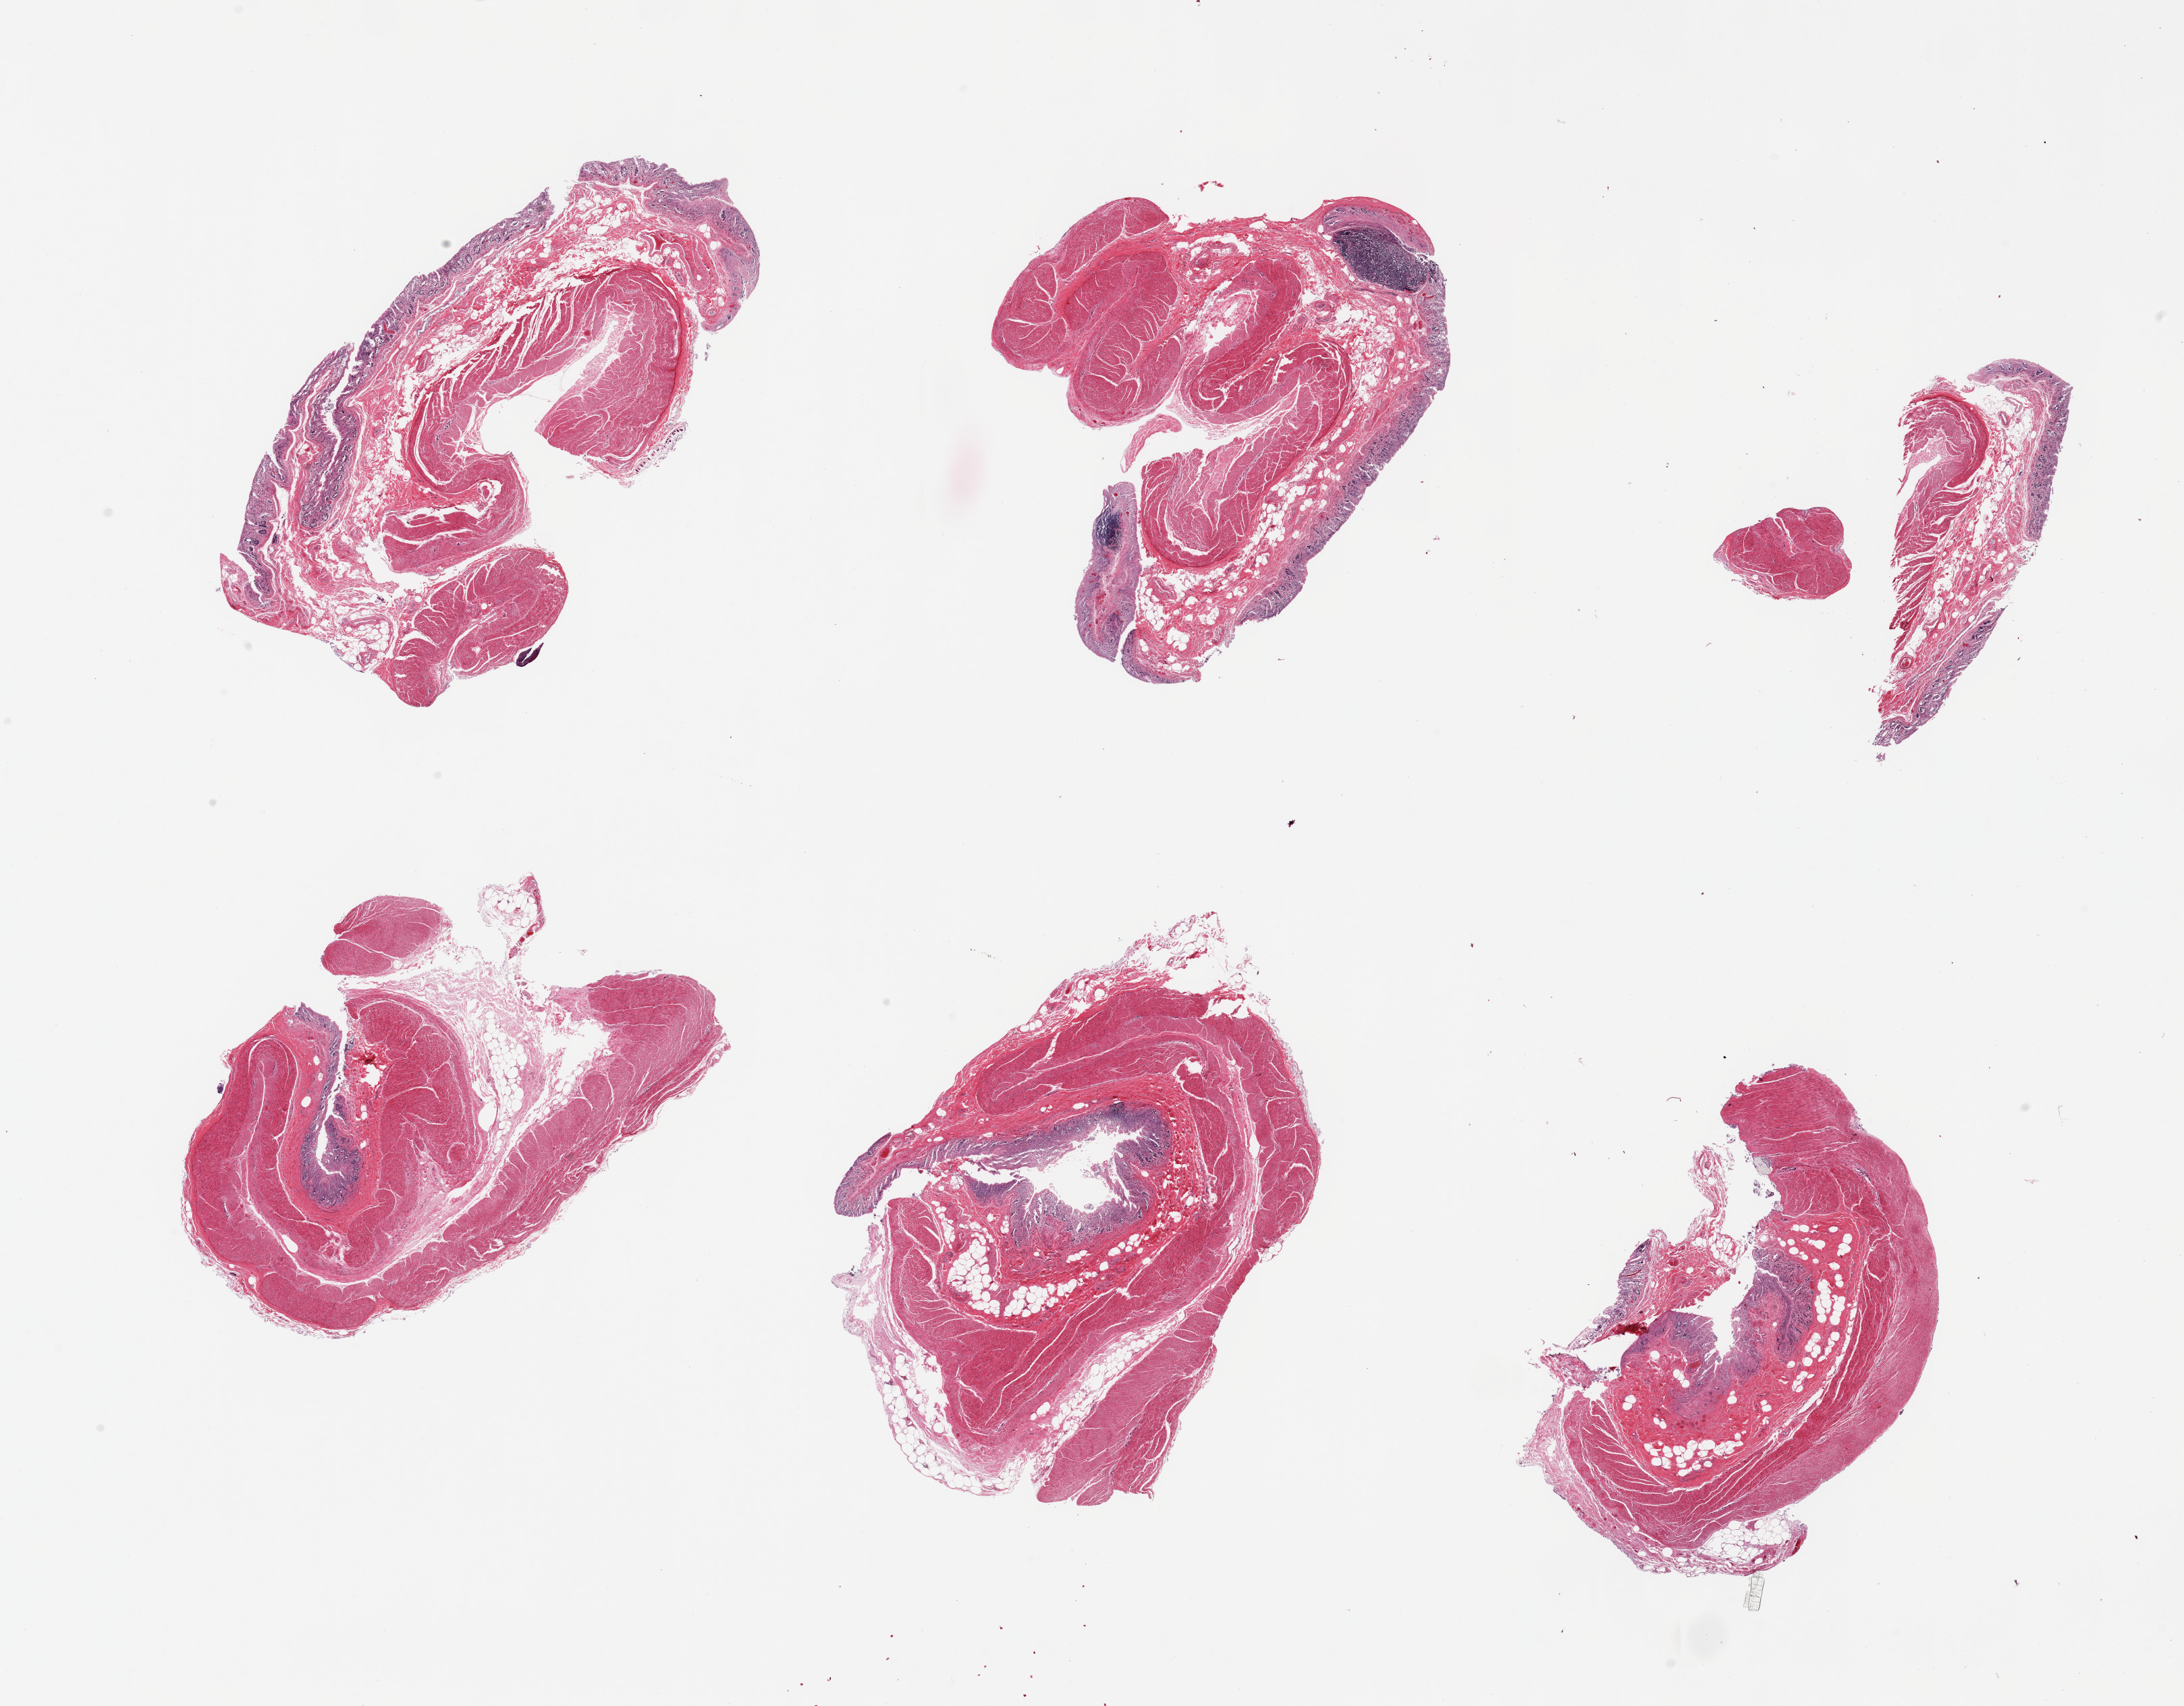
Digitized haematoxylin and eosin-stained section — shown as a low-resolution overview of the whole scanned area (about 25.6 x 20.0 mm); PAXgene-fixed paraffin-embedded (PFPE) section; sampled site (target tissue): transverse colon; donor tissue sample. Male donor.
Reviewer comment on this tissue sample: 6 pieces; full thickness sections, mucosa is severely autolyzed.